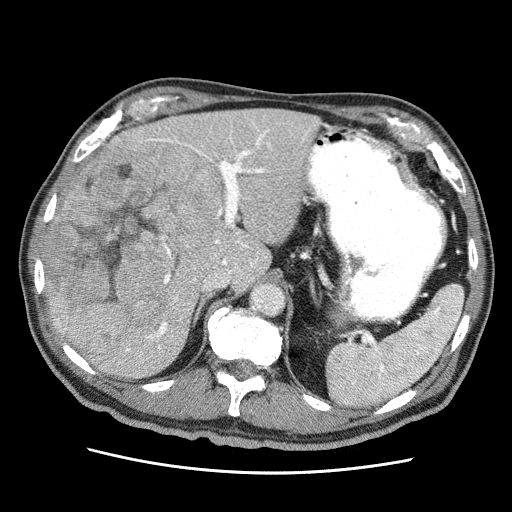
Contrast-enhanced abdominal CT (liver protocol), one axial slice. Position 36 of 75 along the scan axis. Reconstruction kernel STANDARD. 120 kVp. Soft-tissue window (W 400 / L 40 HU). 2.5 mm slice thickness. 512 × 512 image matrix, field of view 360 × 360 mm. From the clinical record (not read from this slice): diagnosis: hepatocellular carcinoma (patient treated with transarterial chemoembolisation; whether this scan precedes or follows treatment is not stated here); TNM stage (as recorded): Stage-IIIA; Child-Pugh class: A.
Outlined on this slice (semi-automatically segmented with operator editing):
- liver parenchyma outside the tumour (the mass and vessels are separate outlines, so this box may not span the whole liver): bounding box (x1, y1, x2, y2) in pixels: (46, 108, 319, 378)
- mass: (48, 135, 222, 343)
- liver vessels: (57, 122, 311, 363)